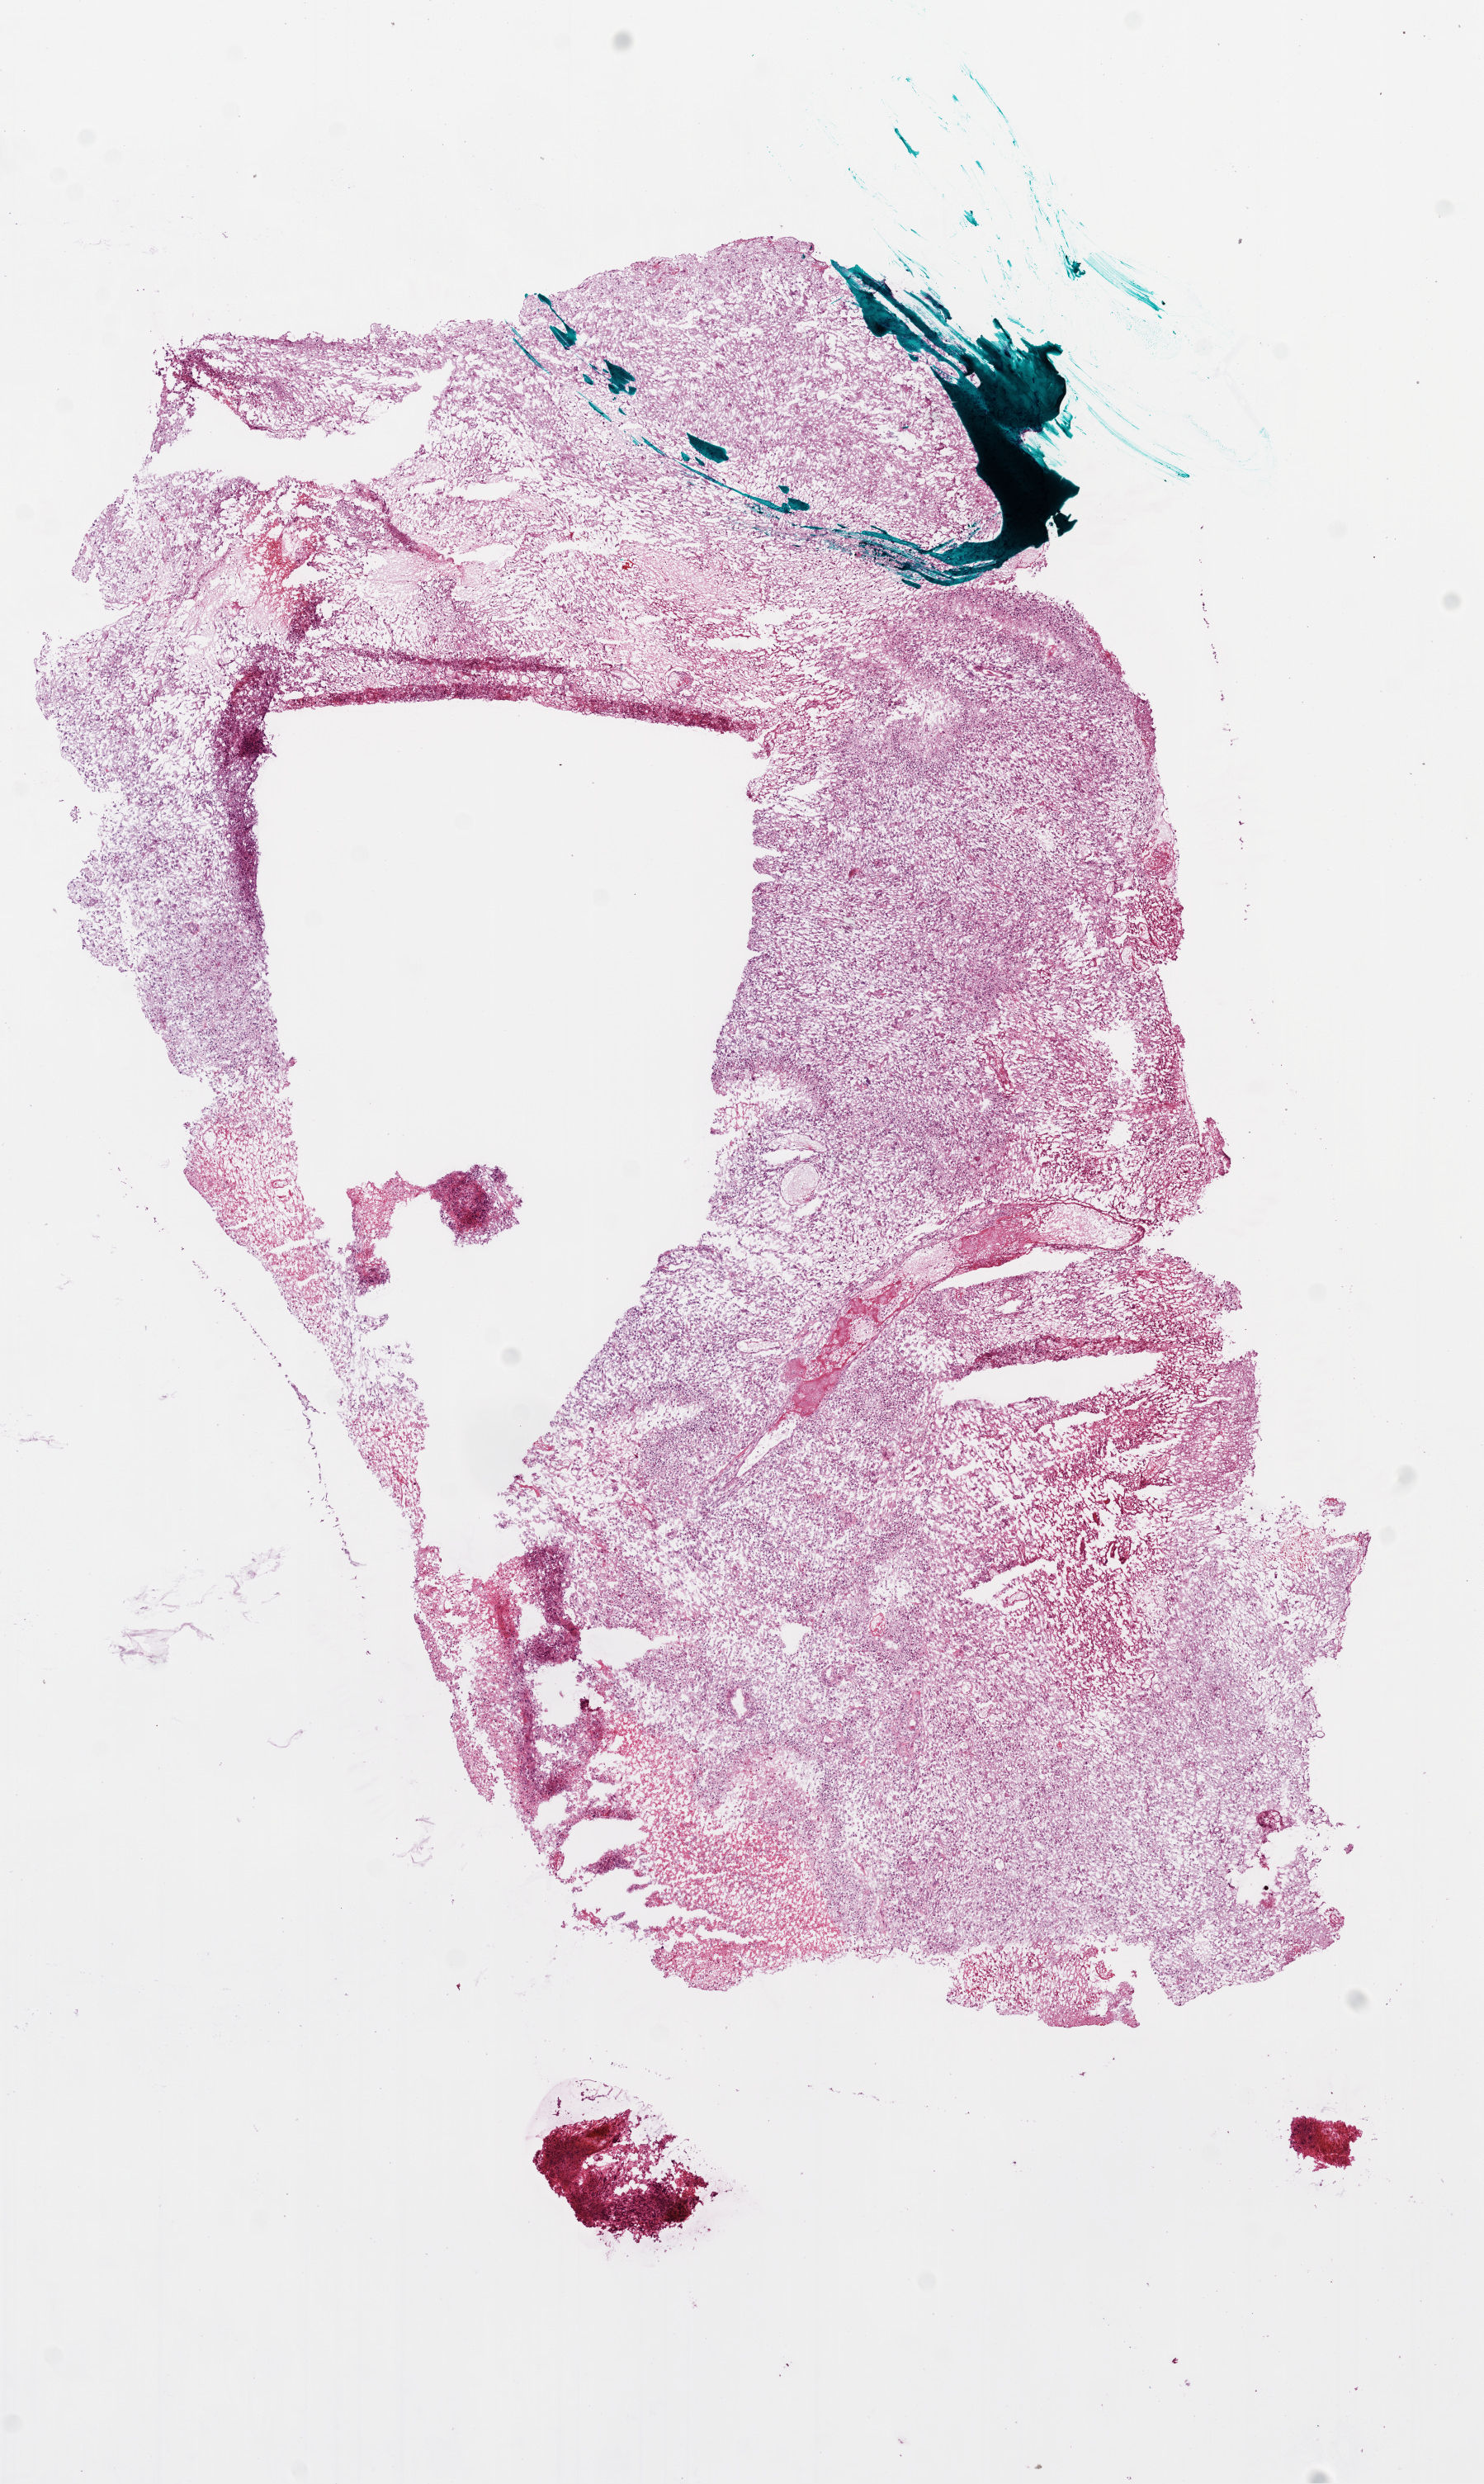
Hematoxylin and eosin (H&E) stained whole-slide image — whole scanned area (about 7.3 x 12.1 mm) shown as a low-resolution overview; frozen section from the bottom of the tissue portion; brain, primary tumour sample. Patient: male, age at initial diagnosis 52 years. Pathologist review of this section (percent, as recorded): tumour cells 60%, tumour nuclei 80%, normal cells 10%, stromal cells 0%, necrosis 30%.
- histologic diagnosis: Glioblastoma